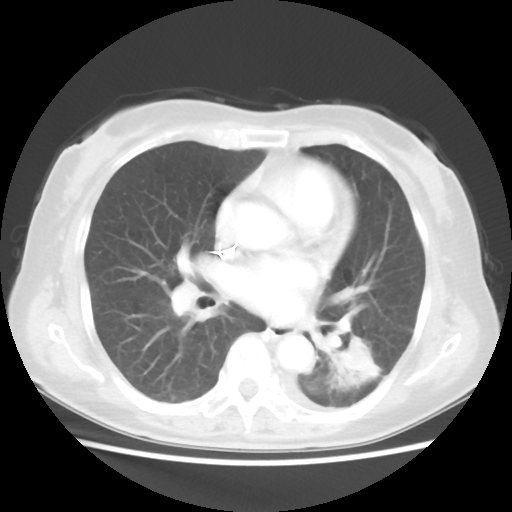
Chest CT, one axial slice. Reconstruction kernel STANDARD. Lung window (W 1500 / L -600 HU). 5 mm slice thickness. 512 × 512 image matrix, field of view 341 × 341 mm. Patient: female, 69 years. Case-level facts recorded for this patient, not image findings: clinical TNM (as recorded): T1c N0 M0.
Outlined on this slice (bounding box drawn by a radiologist):
- lung tumour (recorded histology: adenocarcinoma): bounding box <334,329,387,388> (left, top, right, bottom; pixels)